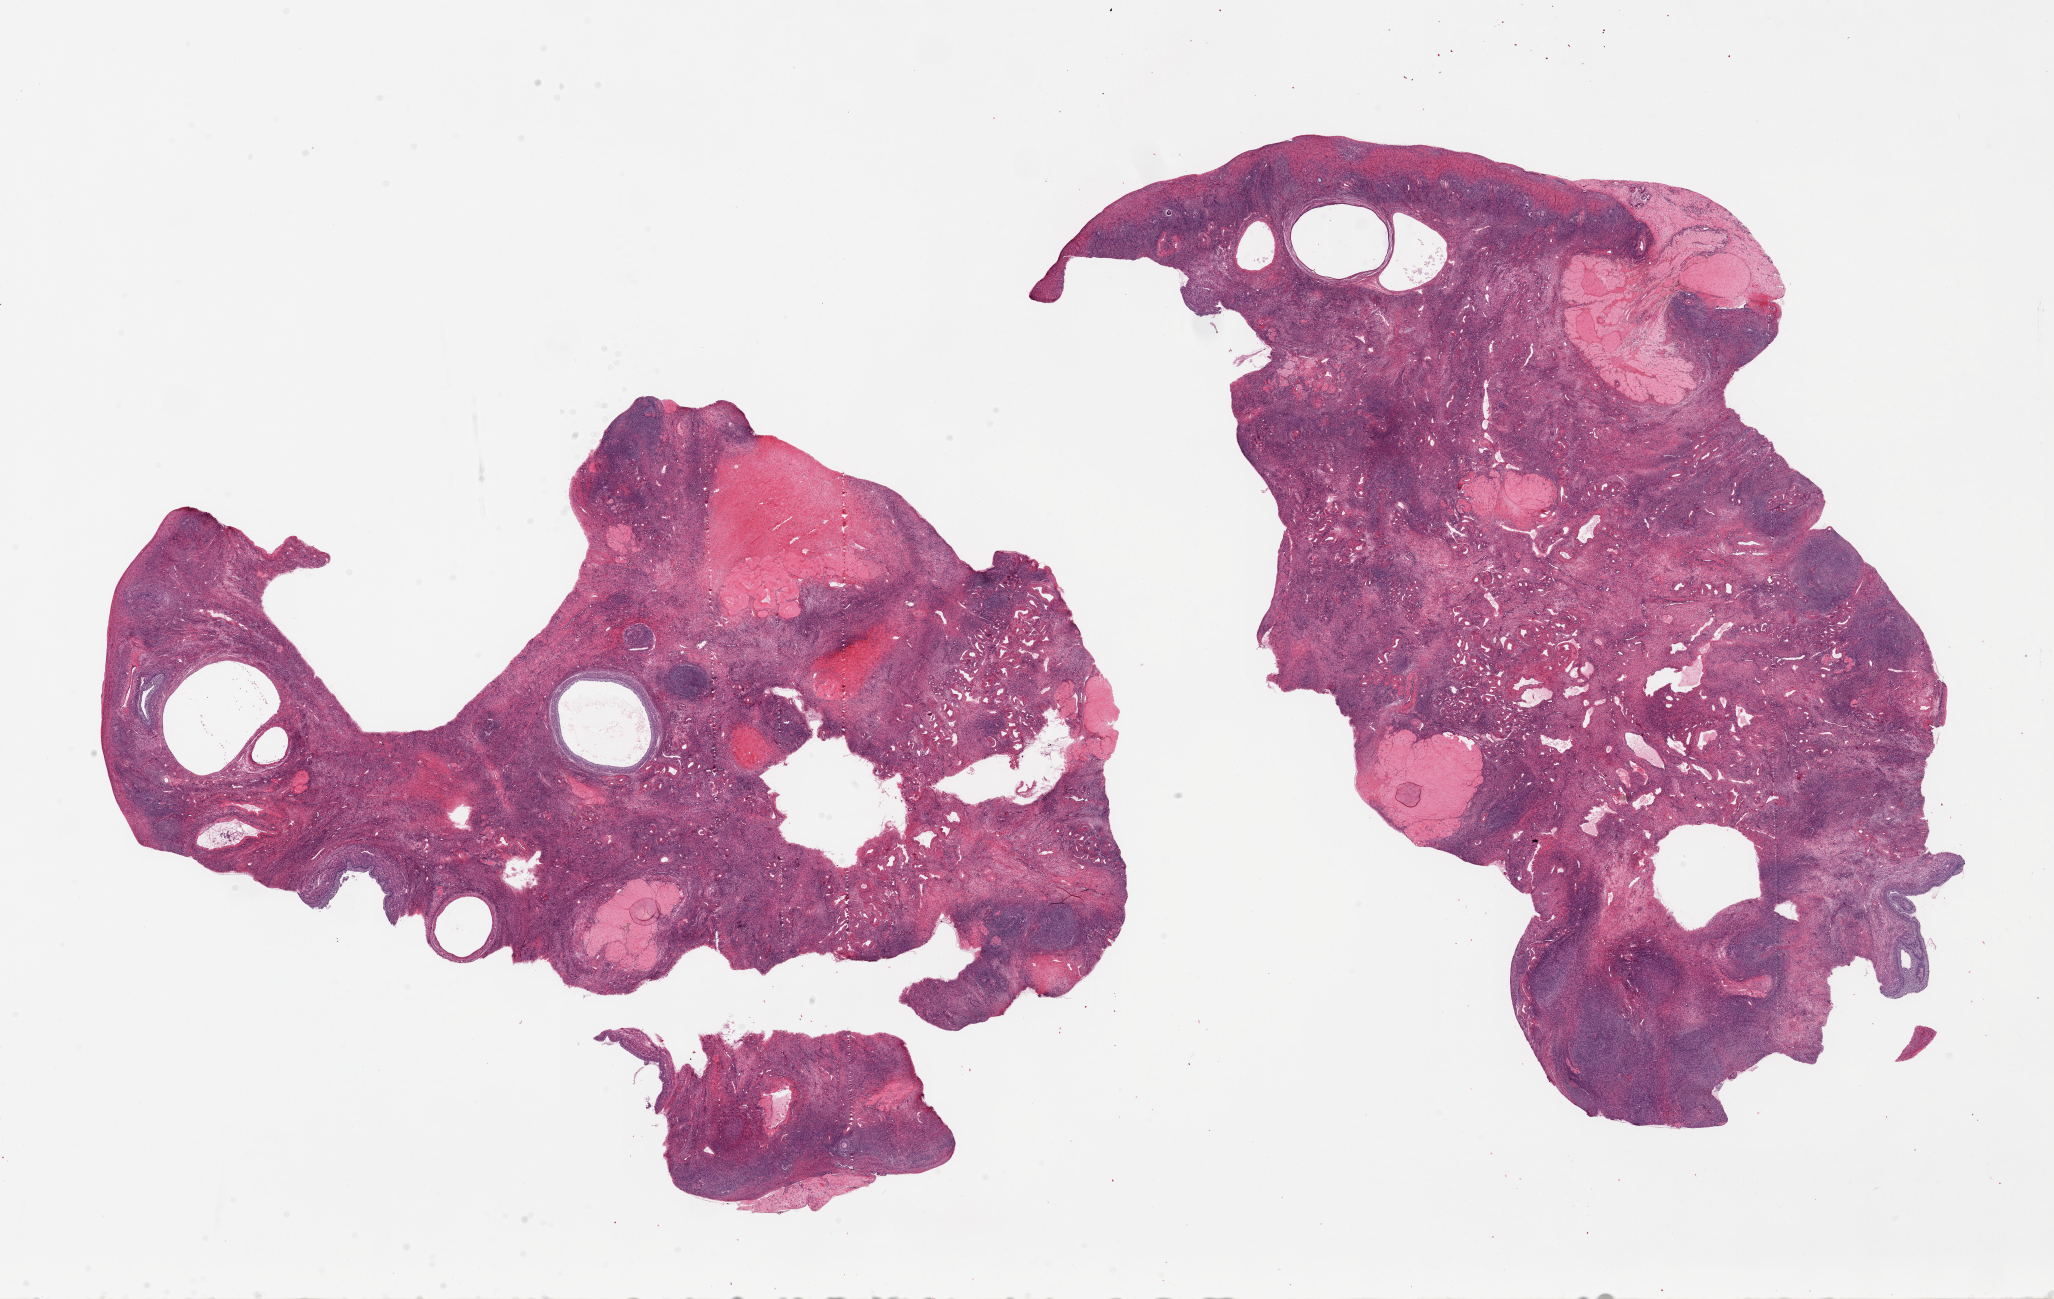
Haematoxylin and eosin whole-slide image, brightfield — shown as a low-resolution overview of the whole scanned area (about 32.5 x 20.5 mm), PAXgene-fixed paraffin-embedded (PFPE) section, section of ovary (target tissue), tissue donor sample. Female donor.
Review note (as recorded): 2 pieces, 17x13mm & 17x10mm; multiple follicular/simple cysts.